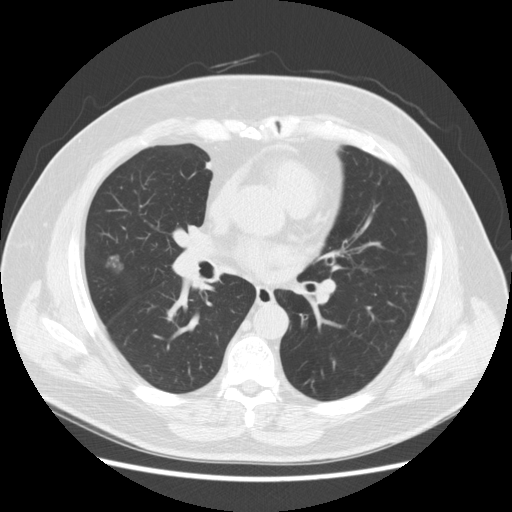
Low-dose screening chest CT, axial slice, first (baseline) screen, lung window (W 1500 / L -600 HU). Male, age 67 years at enrolment.
Expert-annotated lung lesion, bounding box [x1, y1, x2, y2] px = [96, 251, 129, 280]. Screening reader's record for this exam (one nodule recorded; not confirmed to be the boxed lesion): non-calcified nodule or mass ≥4 mm, right middle lobe, 15 × 11 mm, smooth margins, soft tissue attenuation.